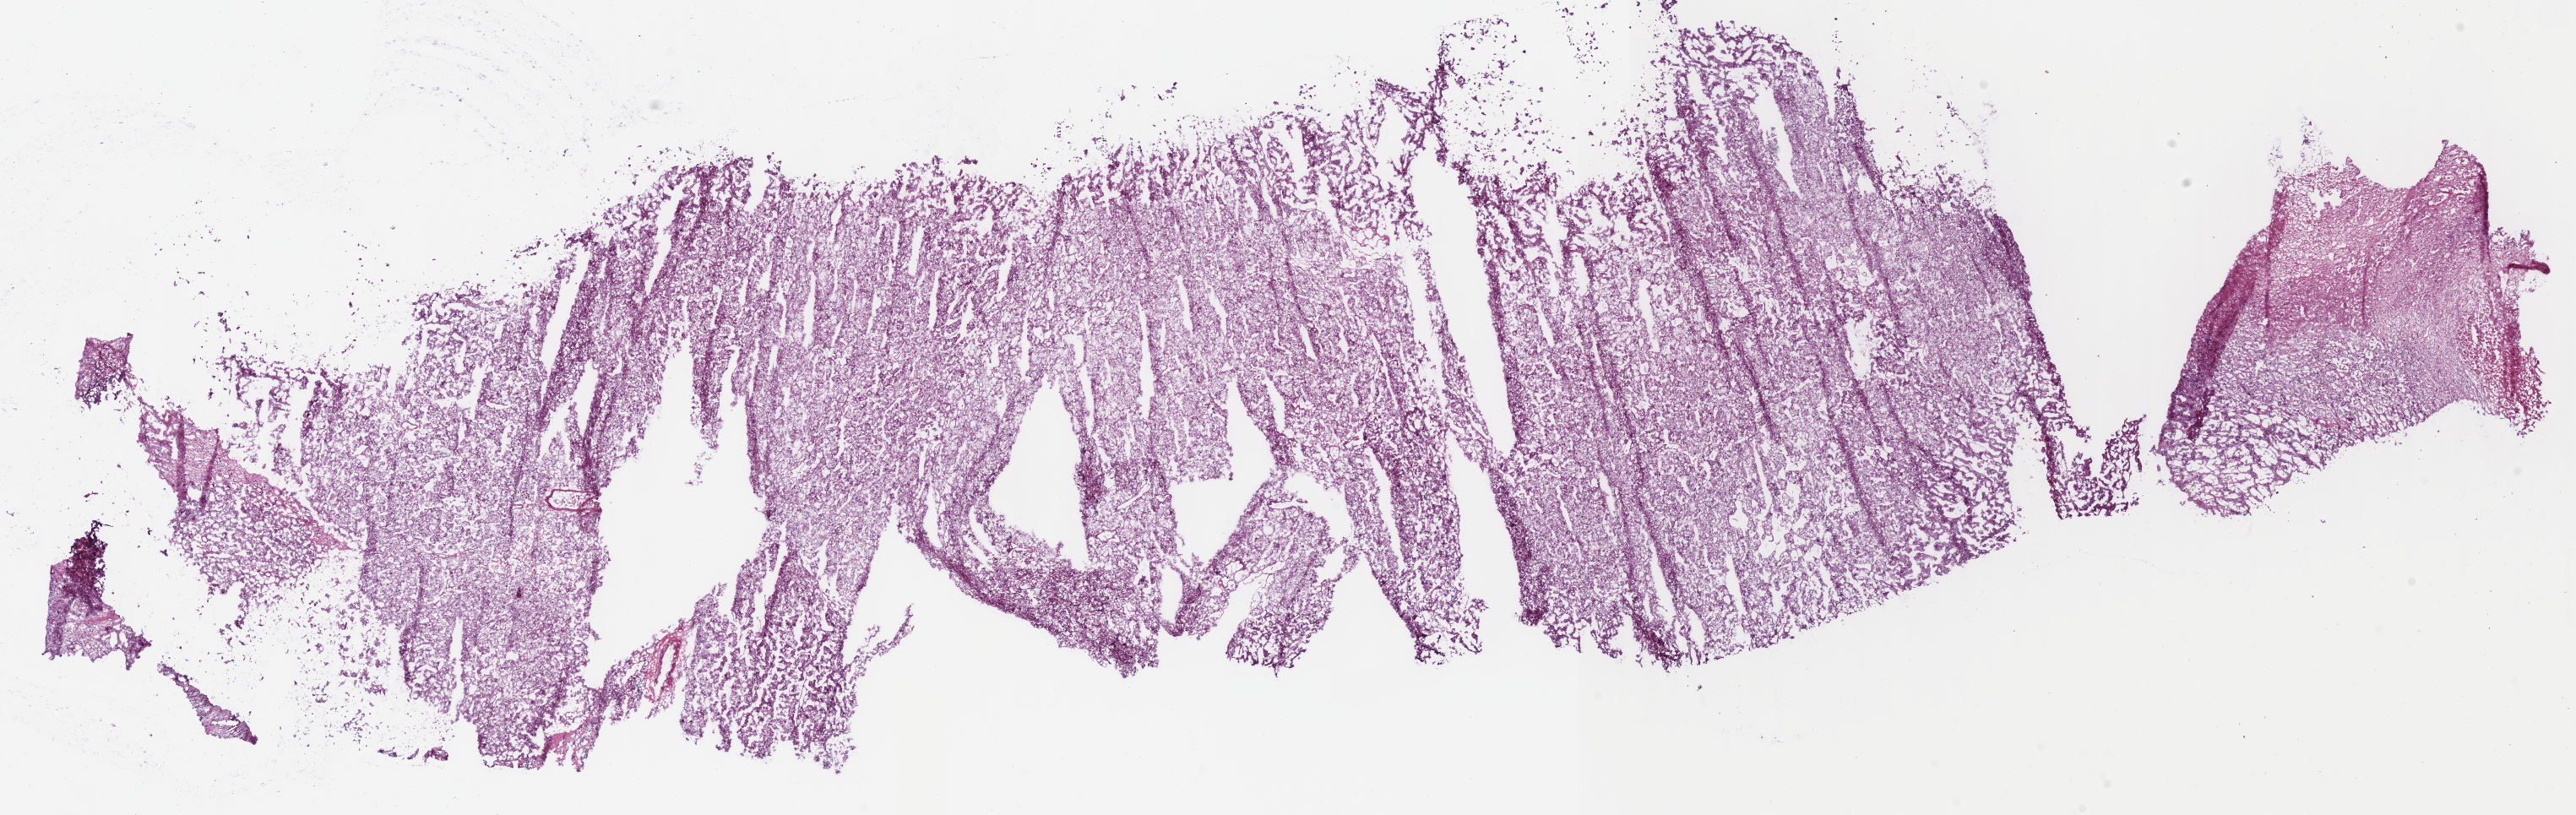
Digitized H&E-stained tissue section (whole slide), low-resolution overview of the scanned area, about 24.0 x 7.6 mm (slide scanned at 40x); frozen section from the bottom of the tissue portion; primary tumour sample from the kidney. Male patient; age at initial diagnosis 46 years.
Pathologic diagnosis: Renal cell carcinoma, chromophobe type.